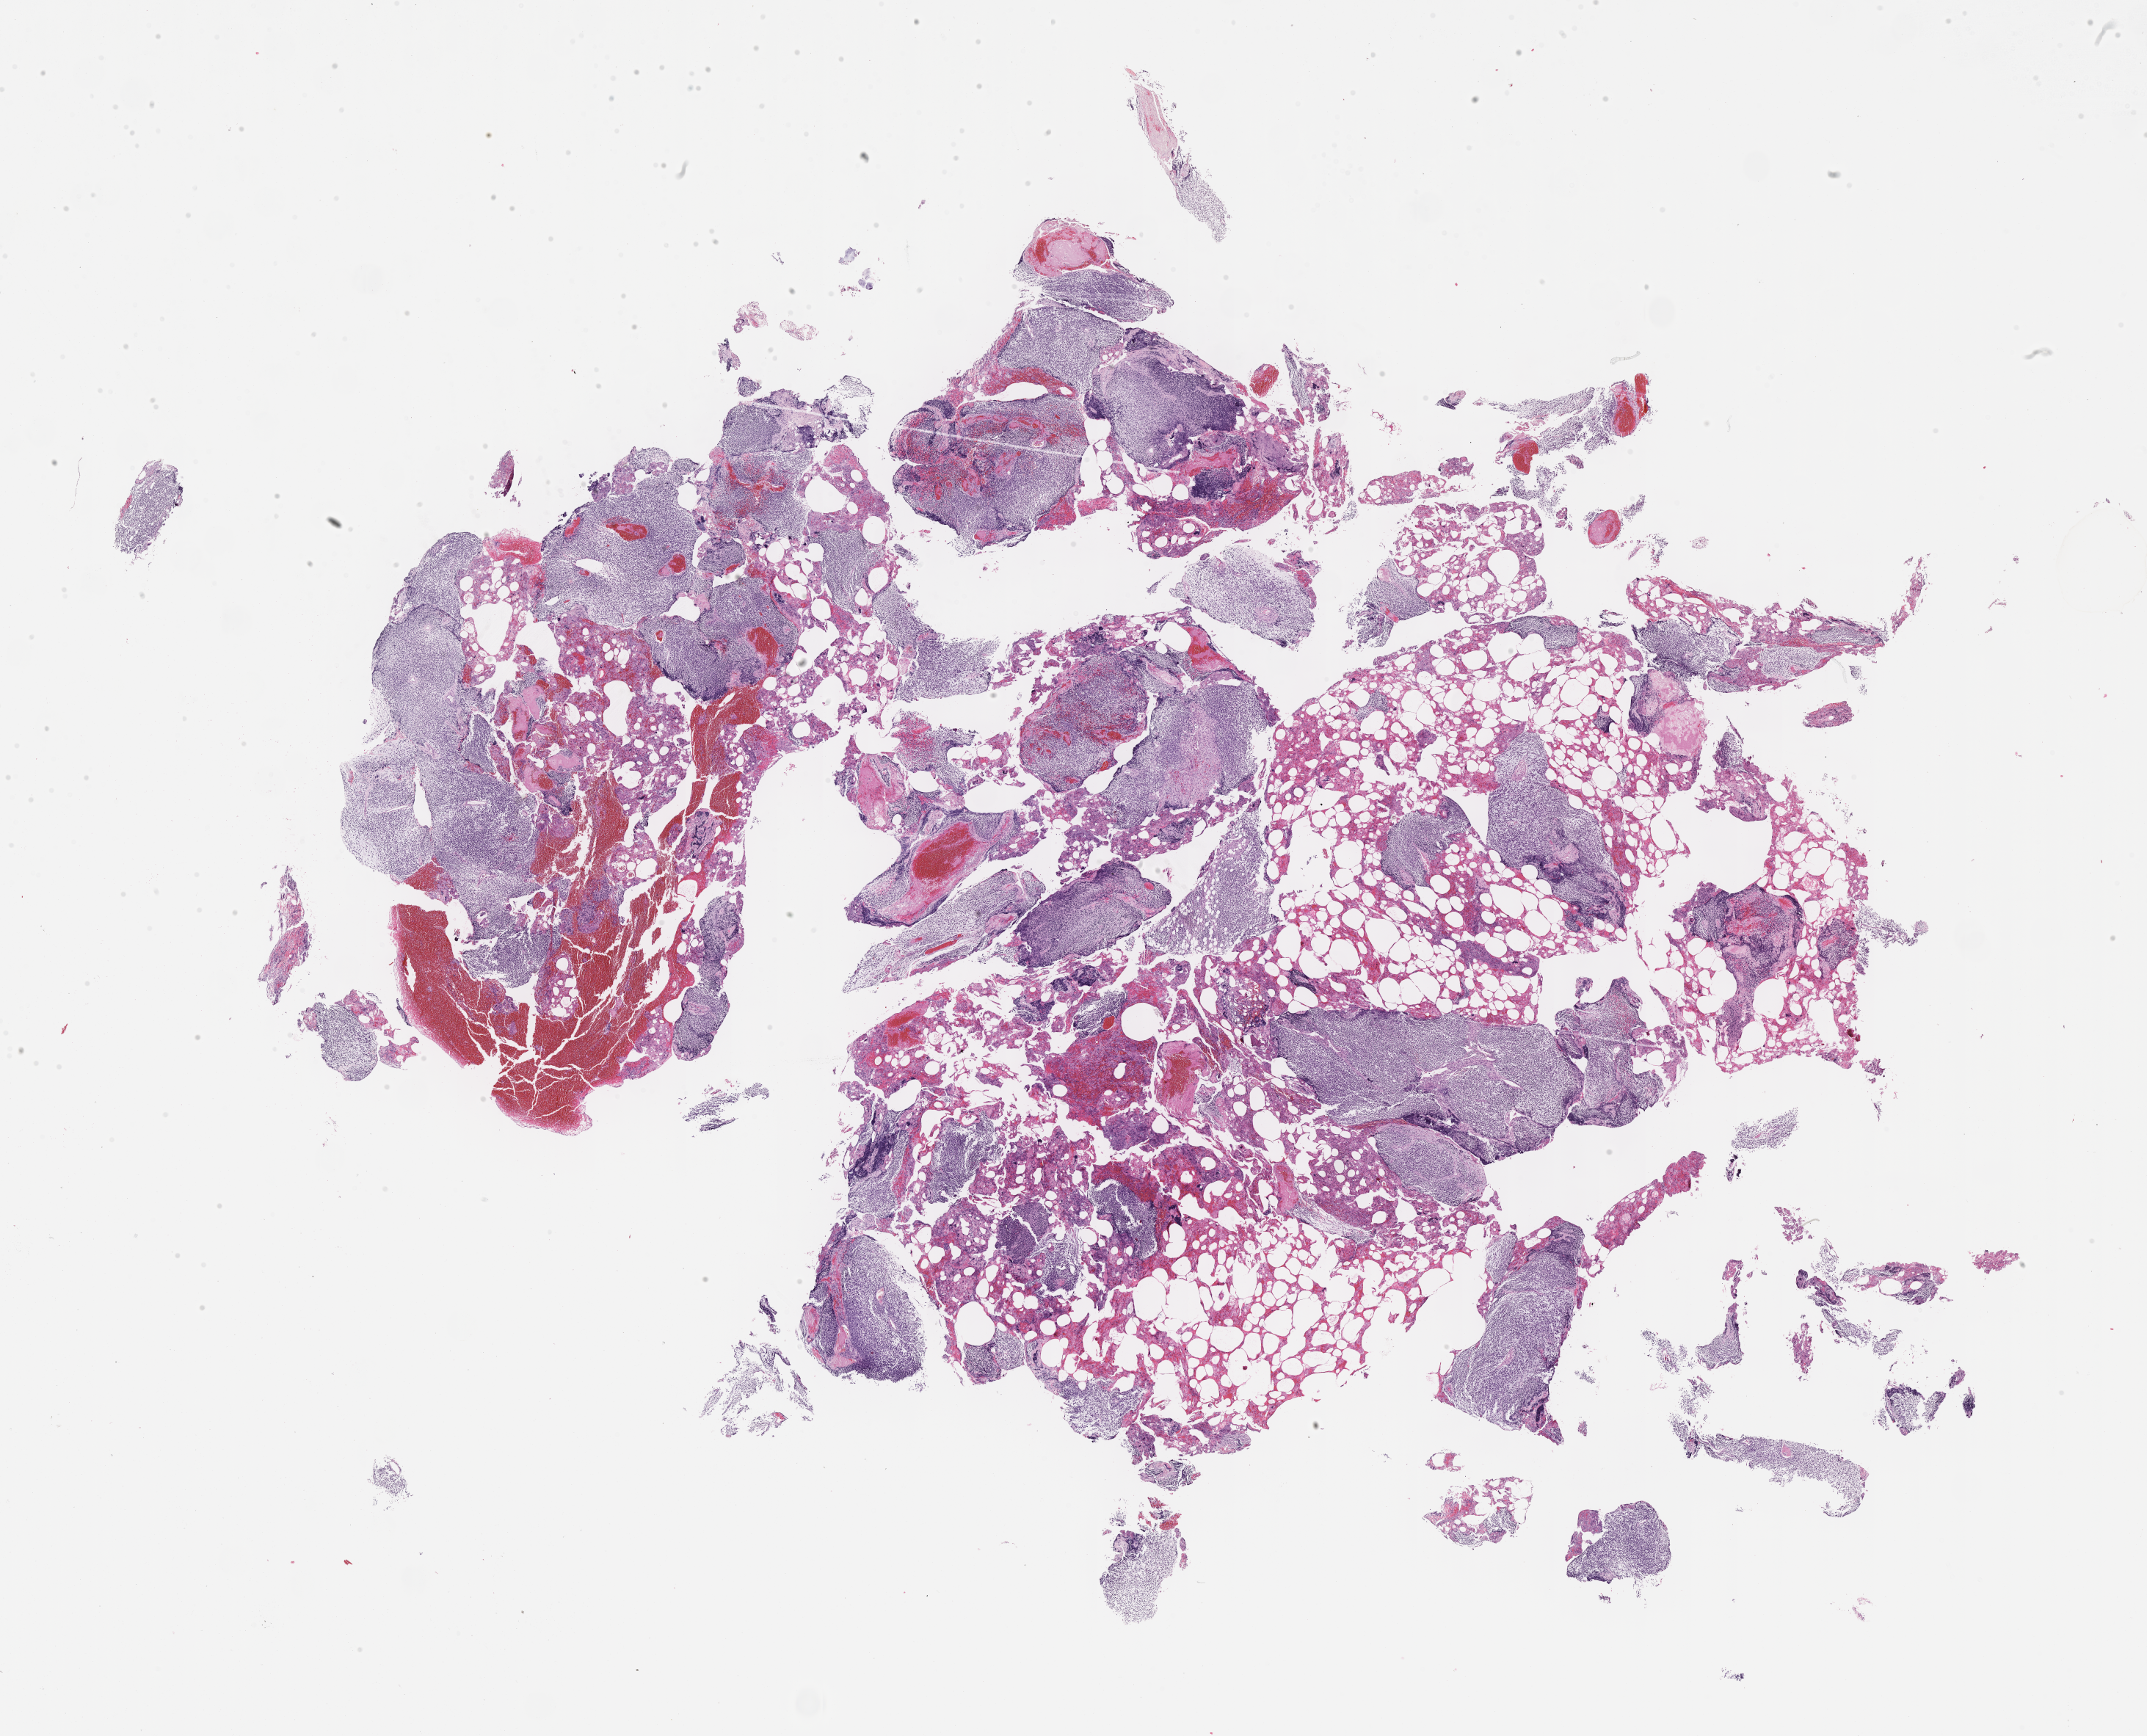
Digitized hematoxylin and eosin (H&E)-stained section of tumor tissue — low-resolution overview of the scanned area, about 23.6 x 19.1 mm; formalin-fixed paraffin-embedded section; sample anatomic site: bone - temporal, infra. Male patient, age at diagnosis 6.4 years.
* metastatic status at presentation (as recorded): non-metastatic (unconfirmed)
* diagnosis: rhabdomyosarcoma; histological classification: embryonal rhabdomyosarcoma
* stage (as recorded): 2
* primary site (case record): paranasal sinus (PM)